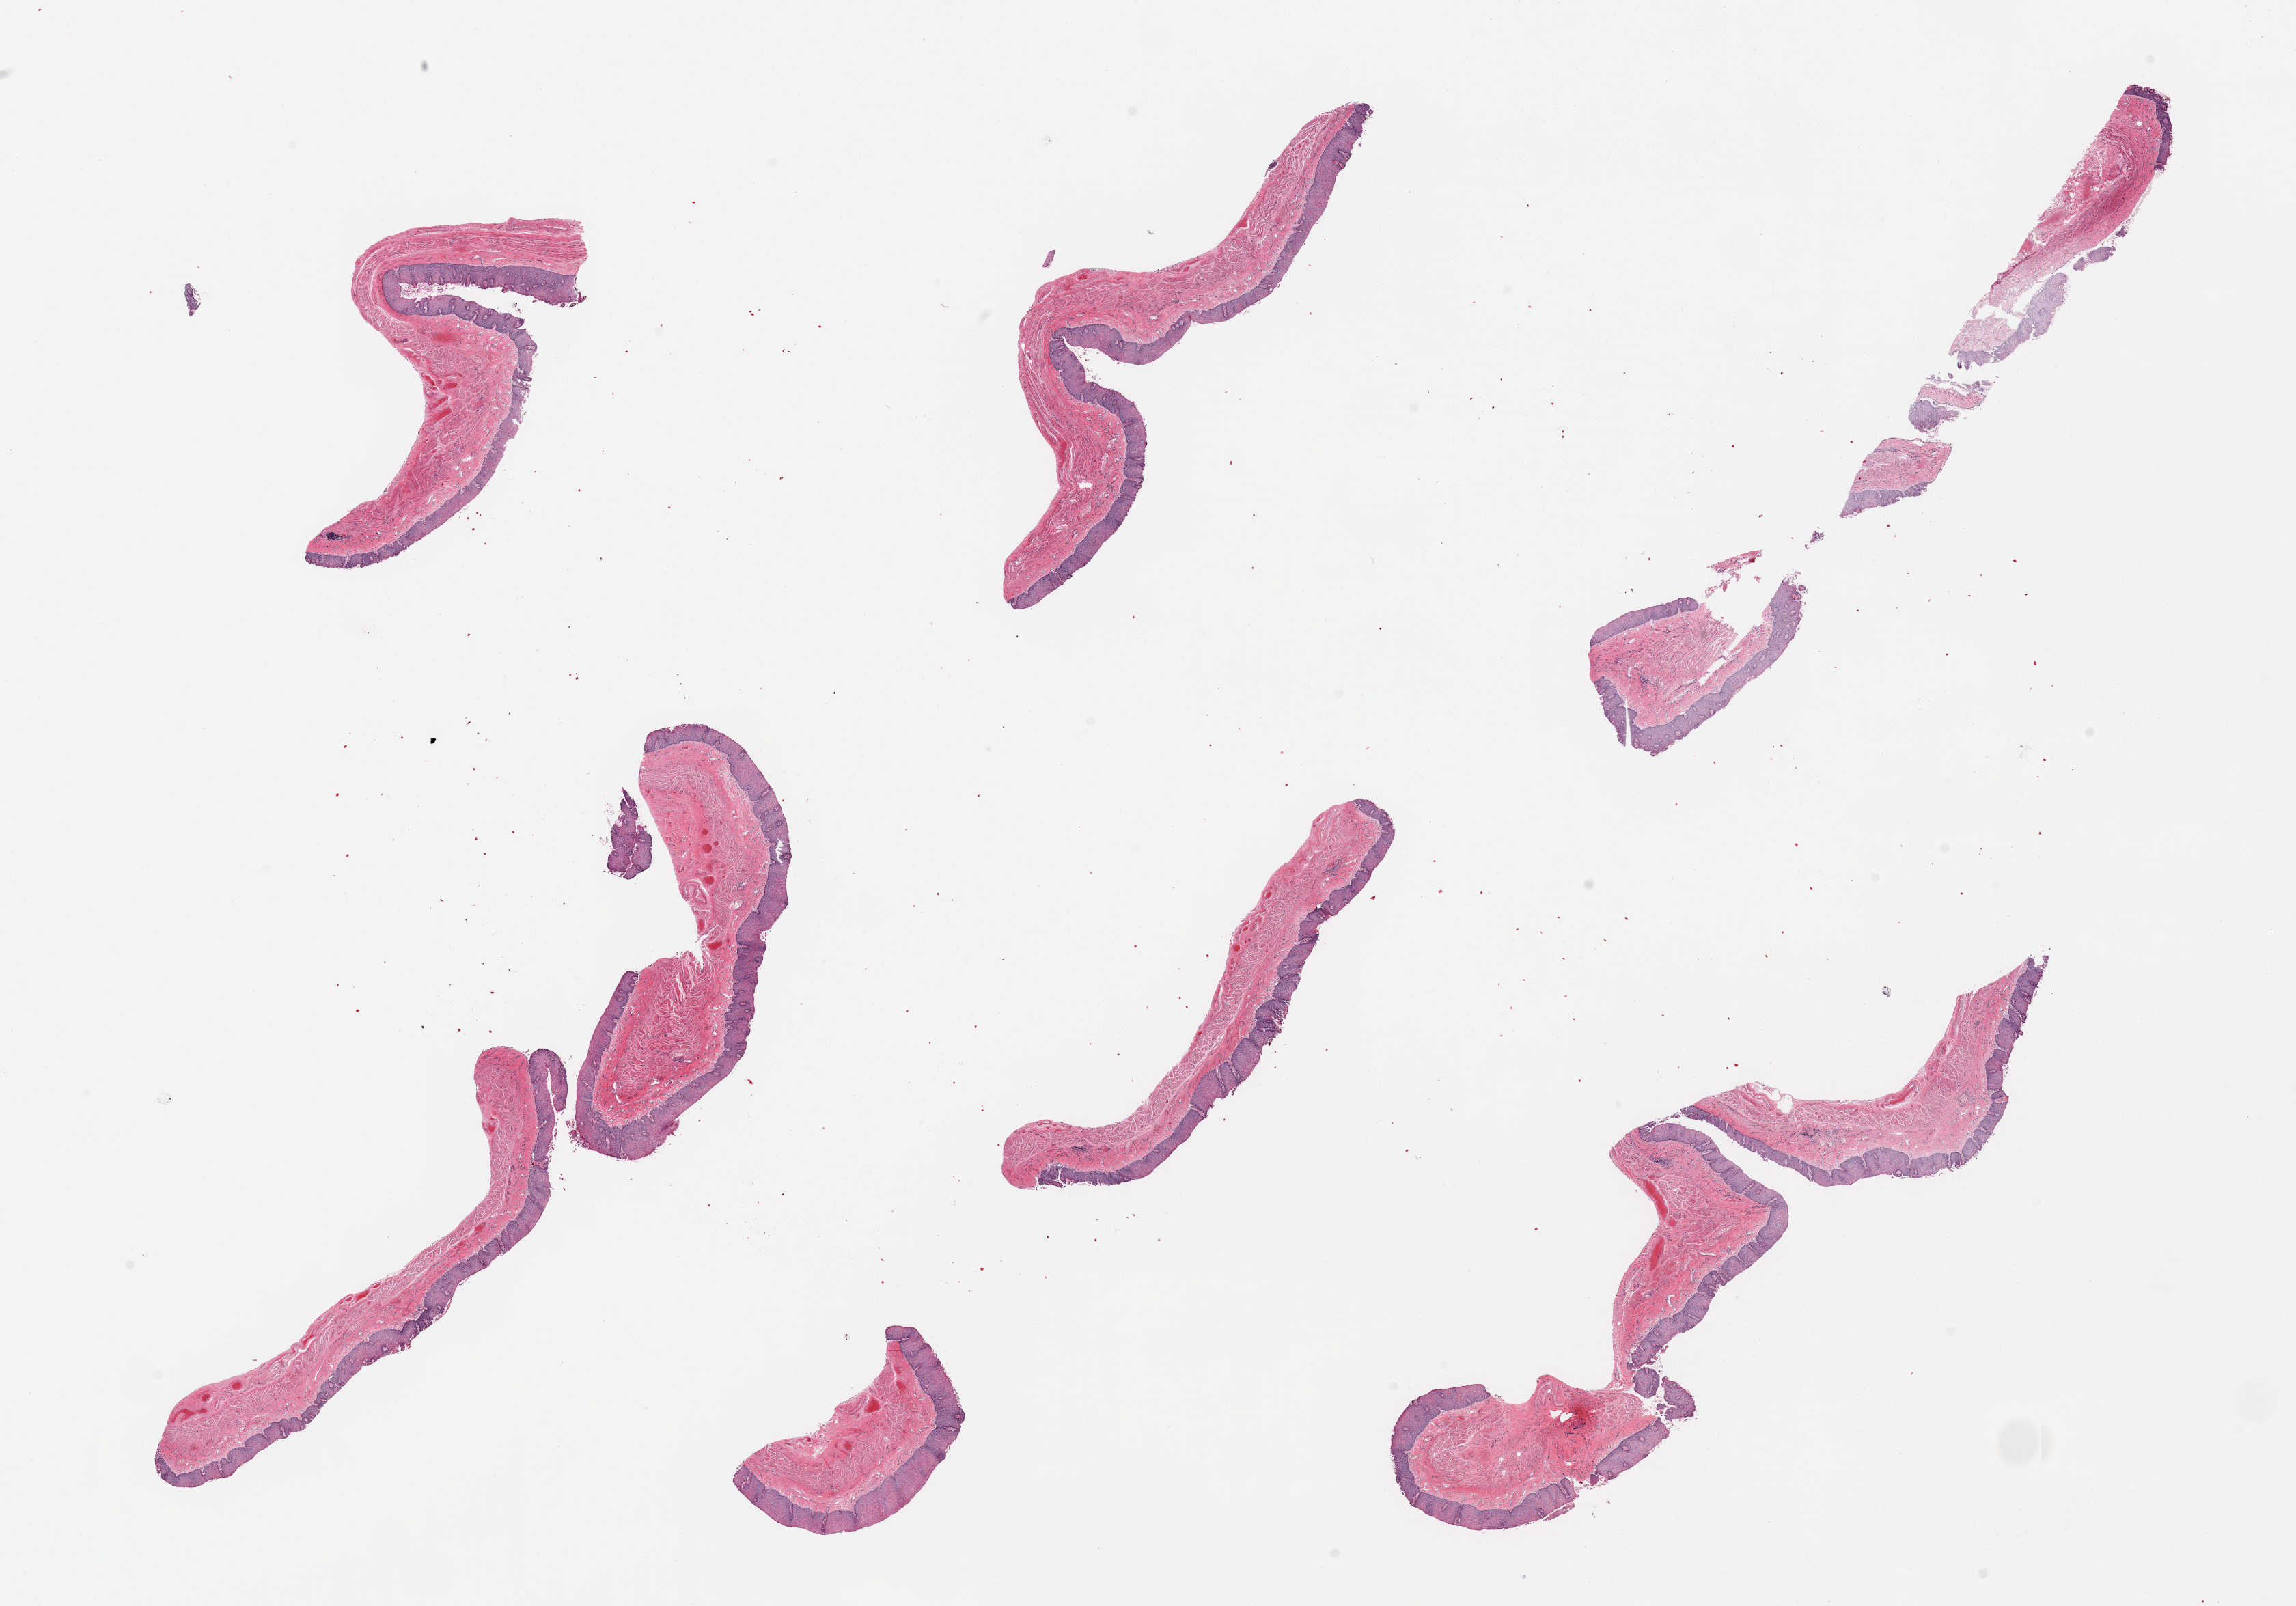
Hematoxylin and eosin (H&E) whole-slide image, low-resolution overview of the scanned area, about 26.6 x 18.6 mm. PAXgene-fixed paraffin-embedded (PFPE) section. Target tissue: esophageal mucous membrane. Donor tissue sample. Female donor.
Pathologist's review note for this sample: 7 pieces (fragmented).